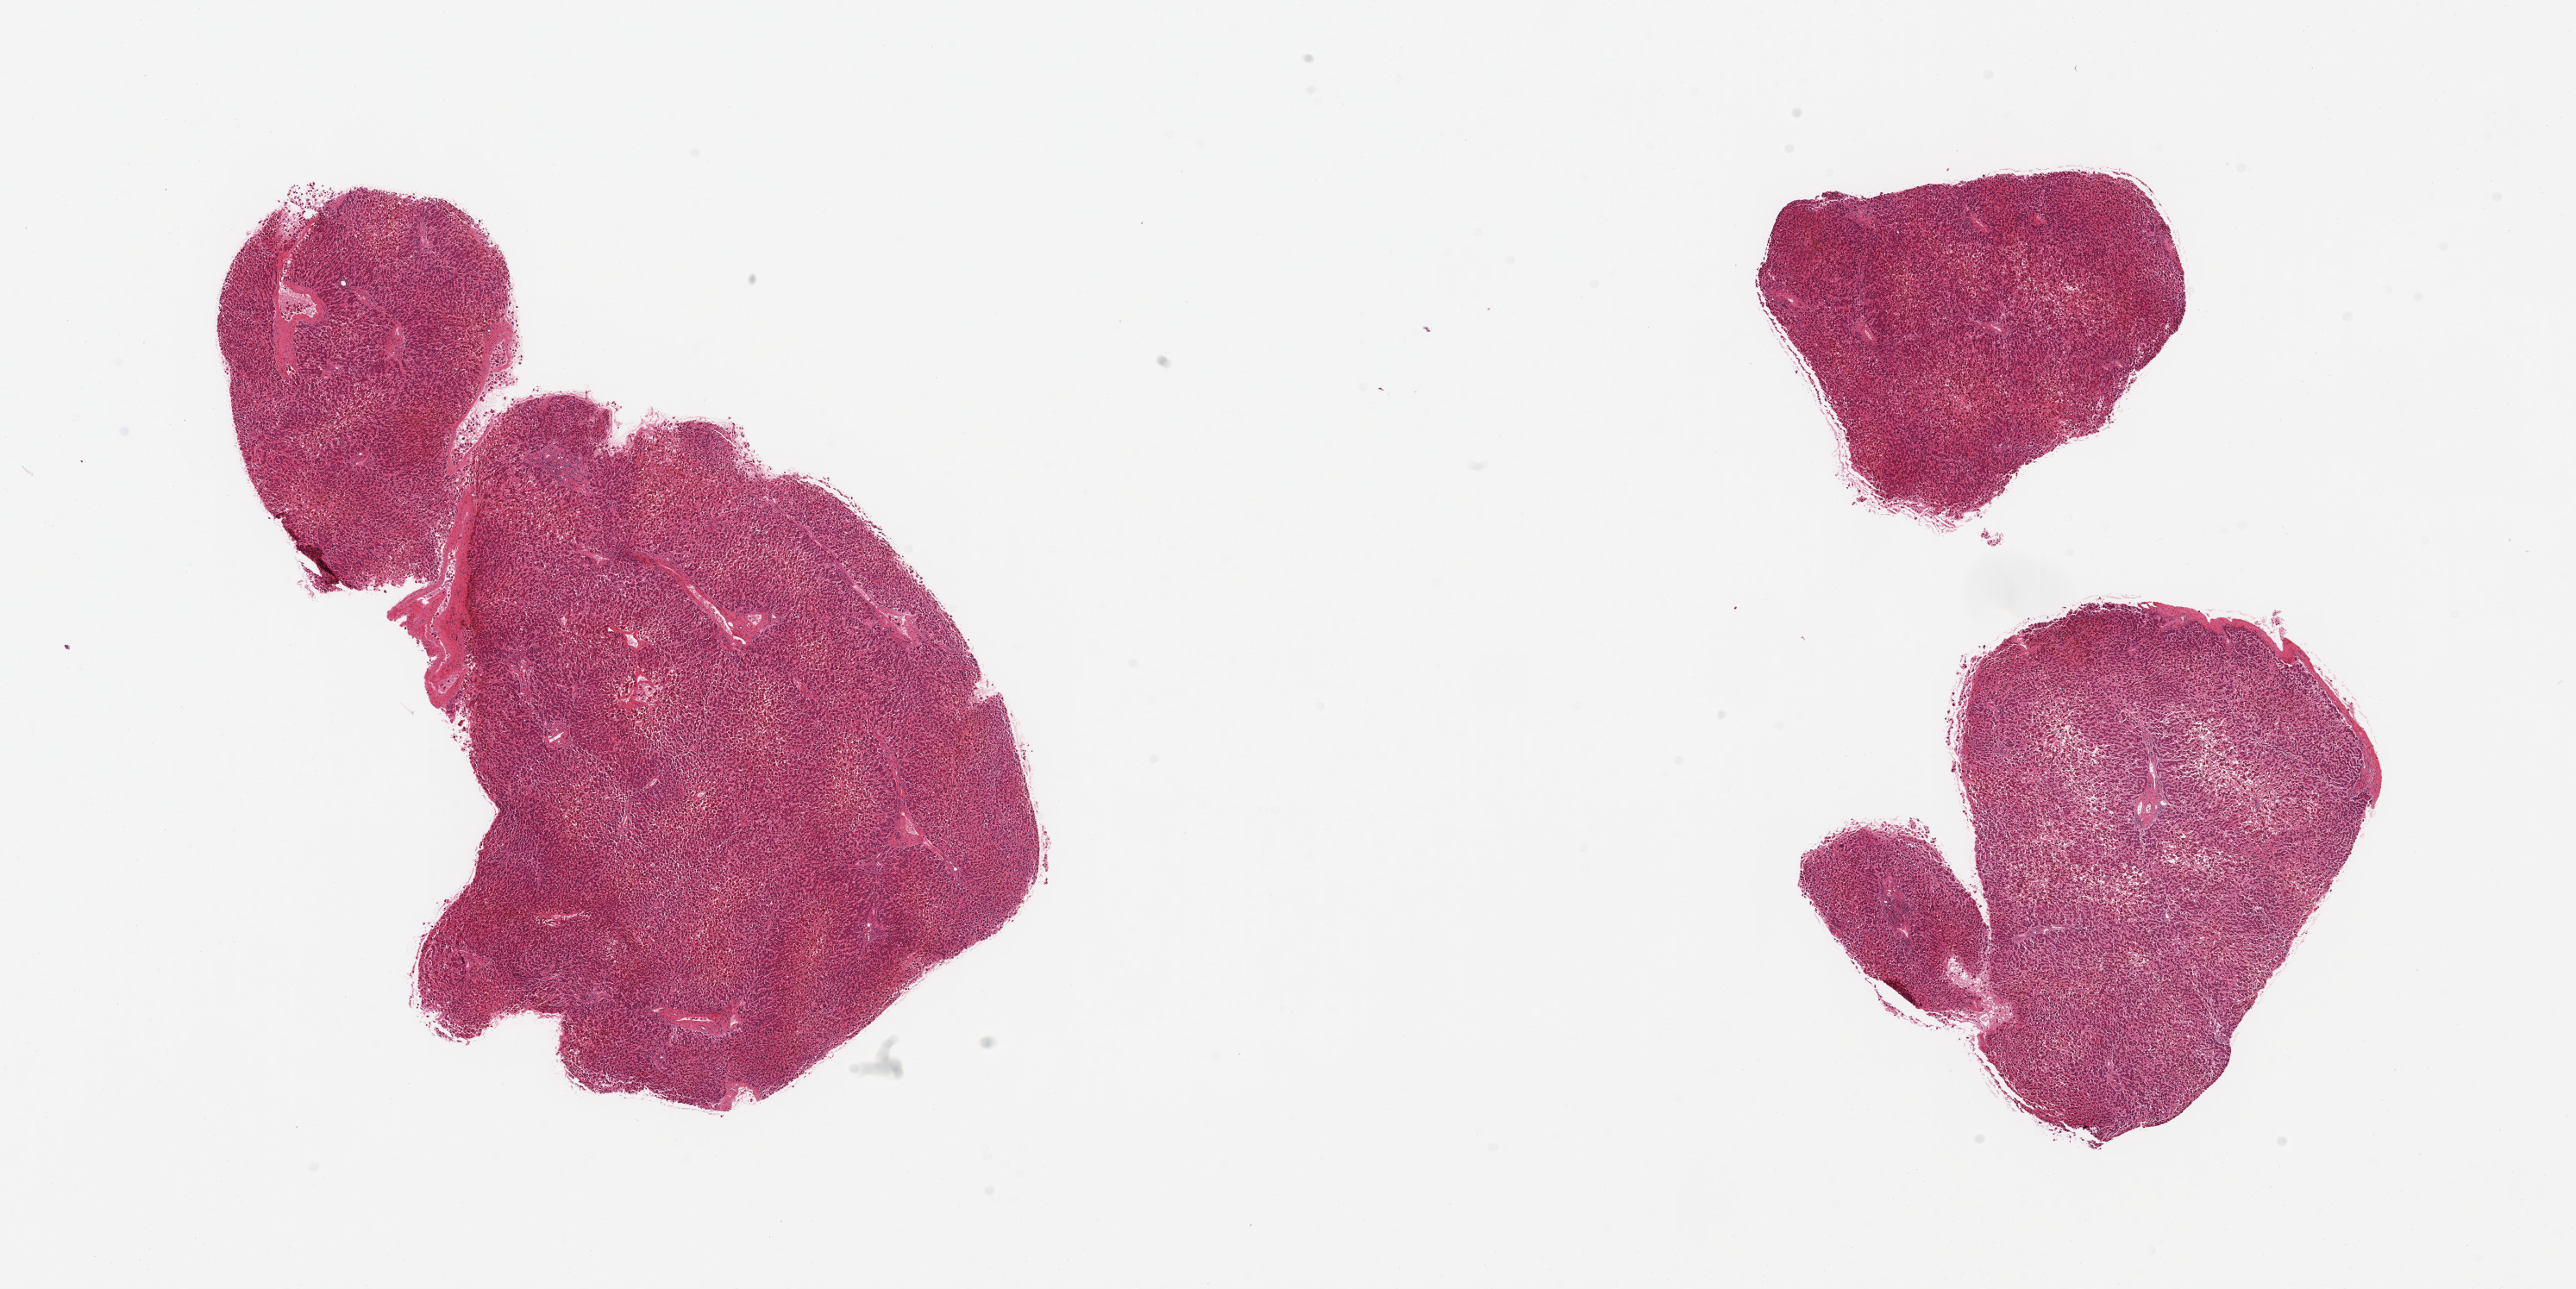
Digitized haematoxylin and eosin-stained section — low-resolution overview of the scanned area, about 23.6 x 11.8 mm. PAXgene-fixed paraffin-embedded (PFPE) section. Target tissue: liver. Tissue donor sample. Donor: male.
- review note (as recorded): 2 pieces, moderate passive congestion